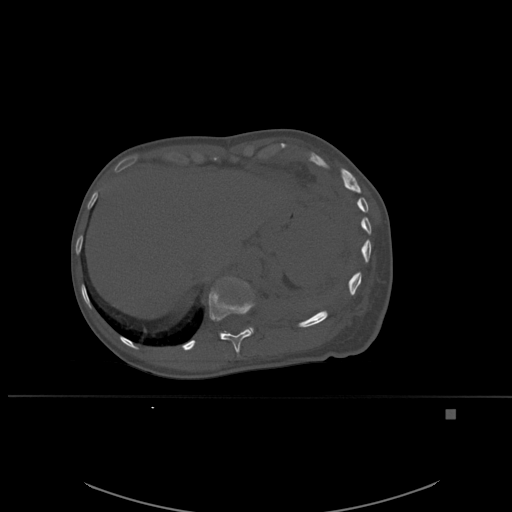
CT including the spine, one axial slice. Slice 295 of 537 in the series (ordered by position). Bone window (W 1800 / L 400 HU). 512 × 512 image matrix. Patient: female, 45 years. Case-level facts recorded for this patient, not image findings: primary cancer: lung.
Structures marked on this image (semi-automatically segmented with operator editing):
- T11 vertebra: bounding box [x1, y1, x2, y2] px = [209, 287, 255, 354]
- T12 vertebra: [216, 277, 254, 332]